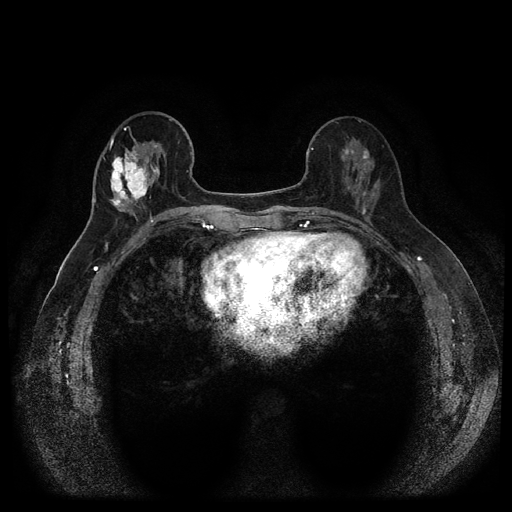
Breast MRI (dynamic contrast-enhanced, multi-phase), one axial slice. Position 41 of 116 along the scan axis. Dynamic contrast-enhanced series, time point 2 of 5 at this slice position (early post-contrast). 1.5 T. TE 2.6 ms, TR 5.4 ms. 2 mm slice thickness. 512 × 512 image matrix. Patient: female, 56 years.
Annotated regions visible in this slice (semi-automatically segmented with operator editing):
- breast lesion (labelled 'tumour' in the annotation; benign lesions carry a separate 'benign' label): bounding box (x1, y1, x2, y2) in pixels: (108, 147, 161, 209)